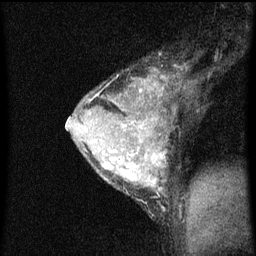
Breast MRI (dynamic contrast-enhanced), one sagittal slice; slice 45 of 60 in the series (ordered by position); dynamic contrast-enhanced series, image 2 of 3 at this slice position (ordered by acquisition); 1.5 T; TE 4.2 ms, TR 8 ms; 2 mm slice thickness; 256 × 256 image matrix, field of view 180 × 180 mm. Patient: female, 33 years.
Structures marked on this image (semi-automatically segmented with operator editing):
- analysis volume of interest (the breast-tissue region the enhancement analysis was run in; not a lesion): bounding box (x1, y1, x2, y2) in pixels: (66, 64, 188, 213)
- tumour enhancement mask (voxels above the 70 % enhancement threshold inside the analysis volume of interest): (67, 80, 165, 187)